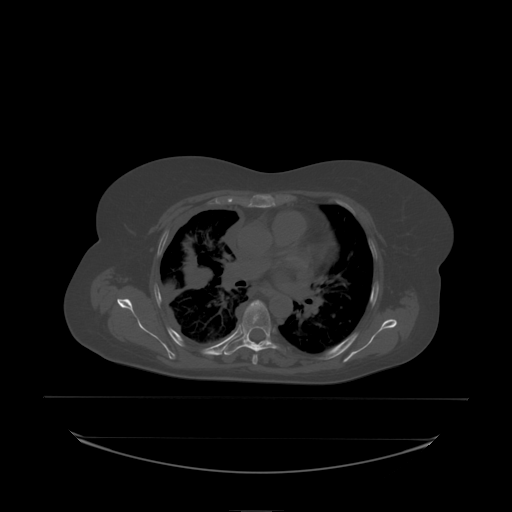
CT including the spine, one axial slice; position 152 of 242 along the scan axis; bone window (W 1800 / L 400 HU); 2.5 mm slice thickness; 512 × 512 image matrix. Female patient, age 53 years. From the clinical record (not read from this slice): primary cancer: lung; vertebrae with lytic lesions (as recorded): T7, L1.
Outlined on this slice (semi-automatically segmented with operator editing):
- T6 vertebra: box from (x=242, y=300) to (x=271, y=338) px